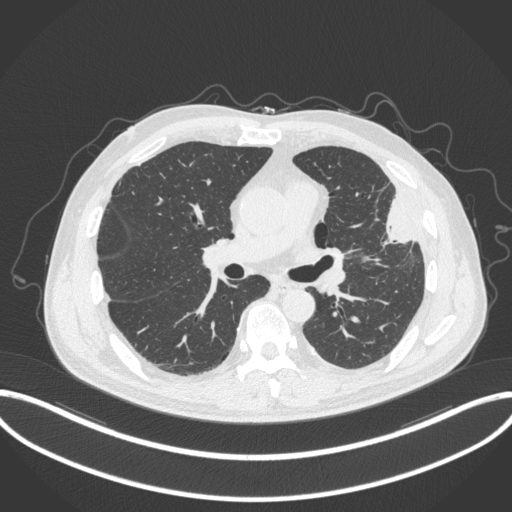
Chest CT, one axial slice. Slice 187 of 382 in the series (ordered by position). Reconstruction kernel B31f. 120 kVp. Lung window (W 1500 / L -600 HU). 1 mm slice thickness. 512 × 512 image matrix. Male patient, age 64 years. From the clinical record (not read from this slice): clinical TNM (as recorded): T4 N1 M0; histopathological grade: G3.
Structures marked on this image (rectangle marked by the reading radiologist):
- lung tumour (recorded histology: adenocarcinoma): bounding box [x1, y1, x2, y2] px = [374, 190, 419, 249]